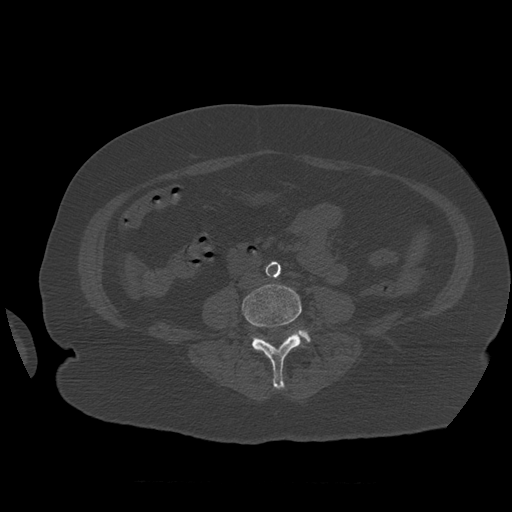
CT including the spine, one axial slice. Position 201 of 399 along the scan axis. Reconstruction kernel STANDARD. Bone window (W 1800 / L 400 HU). 512 × 512 image matrix. Patient age 81 years. Case-level facts recorded for this patient, not image findings: primary cancer: renal; vertebrae with lytic lesions (as recorded): L1.
Structures marked on this image (semi-automatically segmented with operator editing):
- L4 vertebra: bounding box [x1, y1, x2, y2] px = [242, 284, 303, 389]
- L5 vertebra: [251, 330, 311, 344]